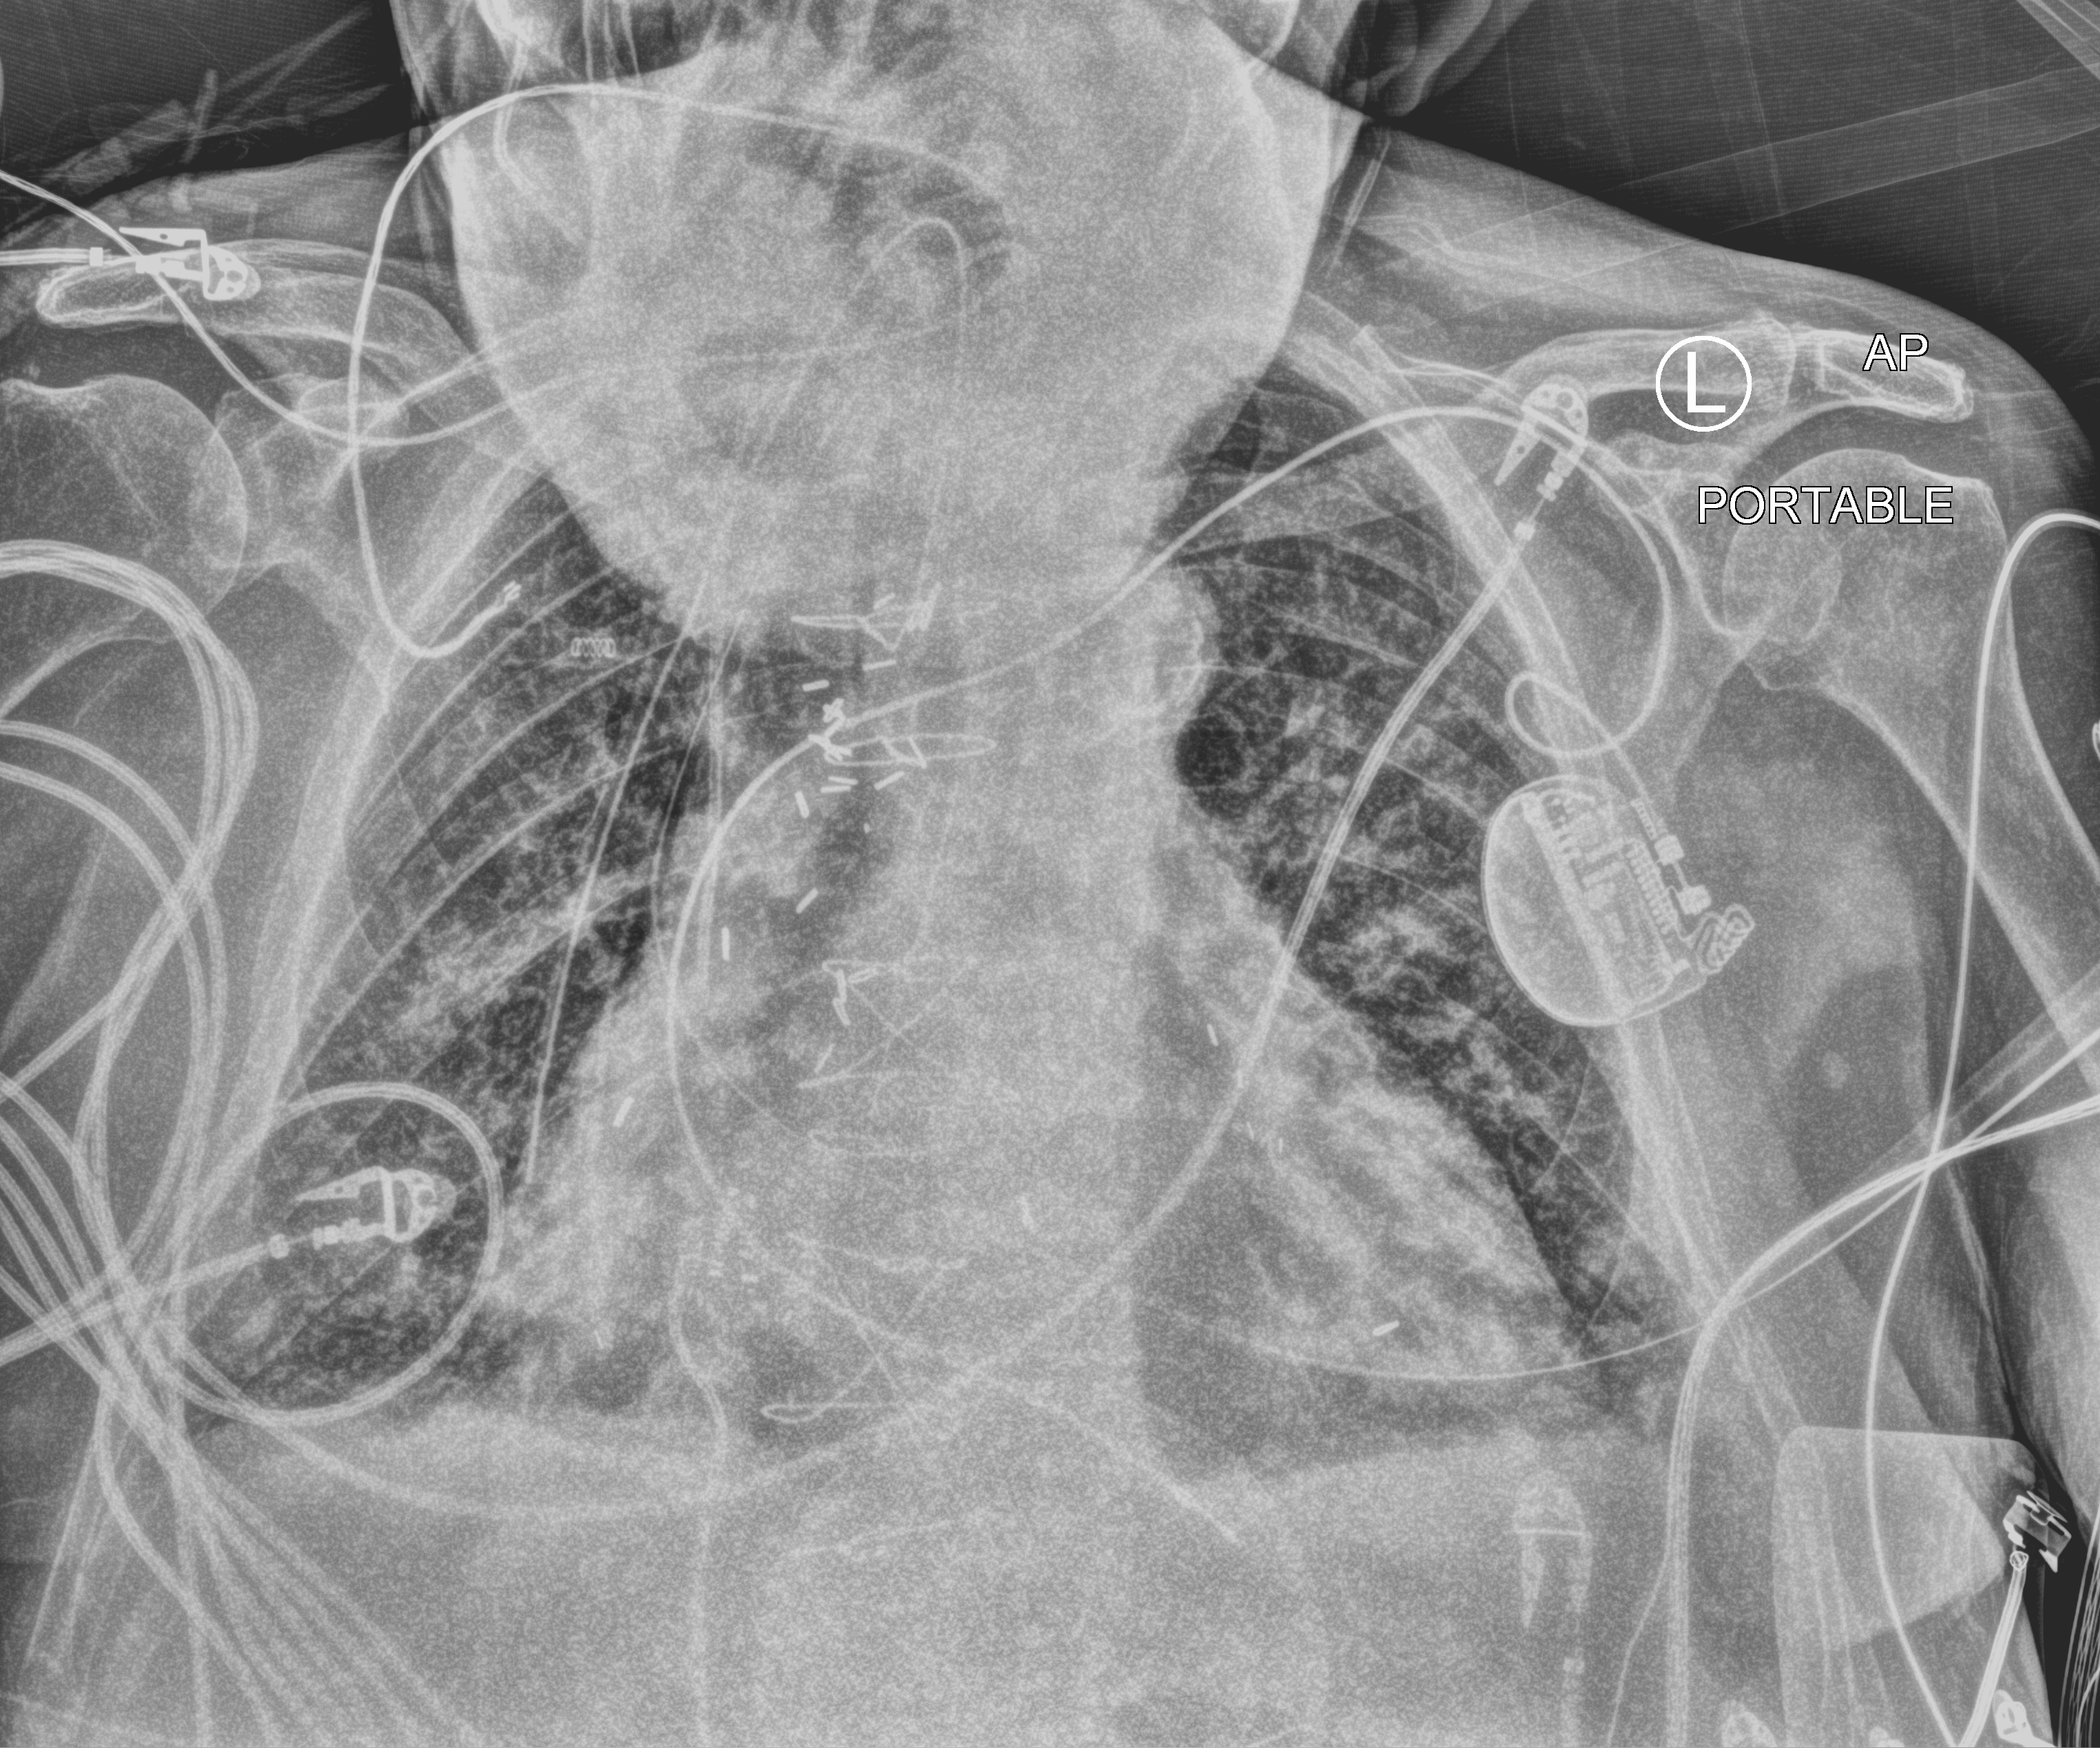
Chest X-ray (portable), anteroposterior (AP) projection. Male patient hospitalised with COVID-19, age 75–90 years.
Hospital-stay facts (about this admission, not read from this image; timing relative to this image not recorded): mechanically ventilated during this hospital stay: yes; smoking status (admission record): former.